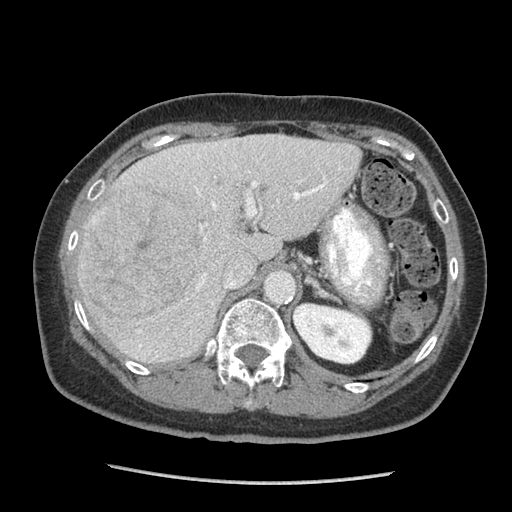
Contrast-enhanced abdominal CT (liver protocol), one axial slice. Slice 57 of 105 in the series (ordered by position). Reconstruction kernel STANDARD. 140 kVp. Soft-tissue window (W 400 / L 40 HU). 2.5 mm slice thickness. 512 × 512 image matrix, field of view 340 × 340 mm. Case-level facts recorded for this patient, not image findings: diagnosis: hepatocellular carcinoma (patient treated with transarterial chemoembolisation; whether this scan precedes or follows treatment is not stated here); TNM stage (as recorded): Stage-I; Child-Pugh class: A; tumour differentiation: moderately differentiated; tumour nodularity: uninodular.
Structures marked on this image (semi-automatically segmented with operator editing):
- liver parenchyma outside the tumour (the mass and vessels are separate outlines, so this box may not span the whole liver): bounding box <76,134,360,362> (left, top, right, bottom; pixels)
- mass: <79,183,215,331>
- liver vessels: <138,143,325,347>